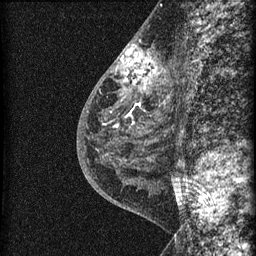
Breast MRI (dynamic contrast-enhanced), one sagittal slice. Dynamic contrast-enhanced series, image 2 of 3 at this slice position (ordered by acquisition). 1.5 T. TE 4.2 ms, TR 22.7 ms. 1.5 mm slice thickness. 256 × 256 image matrix. Patient: female, 48 years. Case-level facts recorded for this patient, not image findings: setting: breast cancer imaged before/during neoadjuvant chemotherapy; receptor status: triple-negative.
Structures marked on this image (semi-automatic segmentation, software-assisted and operator-edited):
- analysis volume of interest (the breast-tissue region the enhancement analysis was run in; not a lesion): box from (x=115, y=34) to (x=169, y=162) px
- tumour enhancement mask (voxels above the 90 % enhancement threshold inside the analysis volume of interest): (x=119, y=44)–(x=159, y=90)